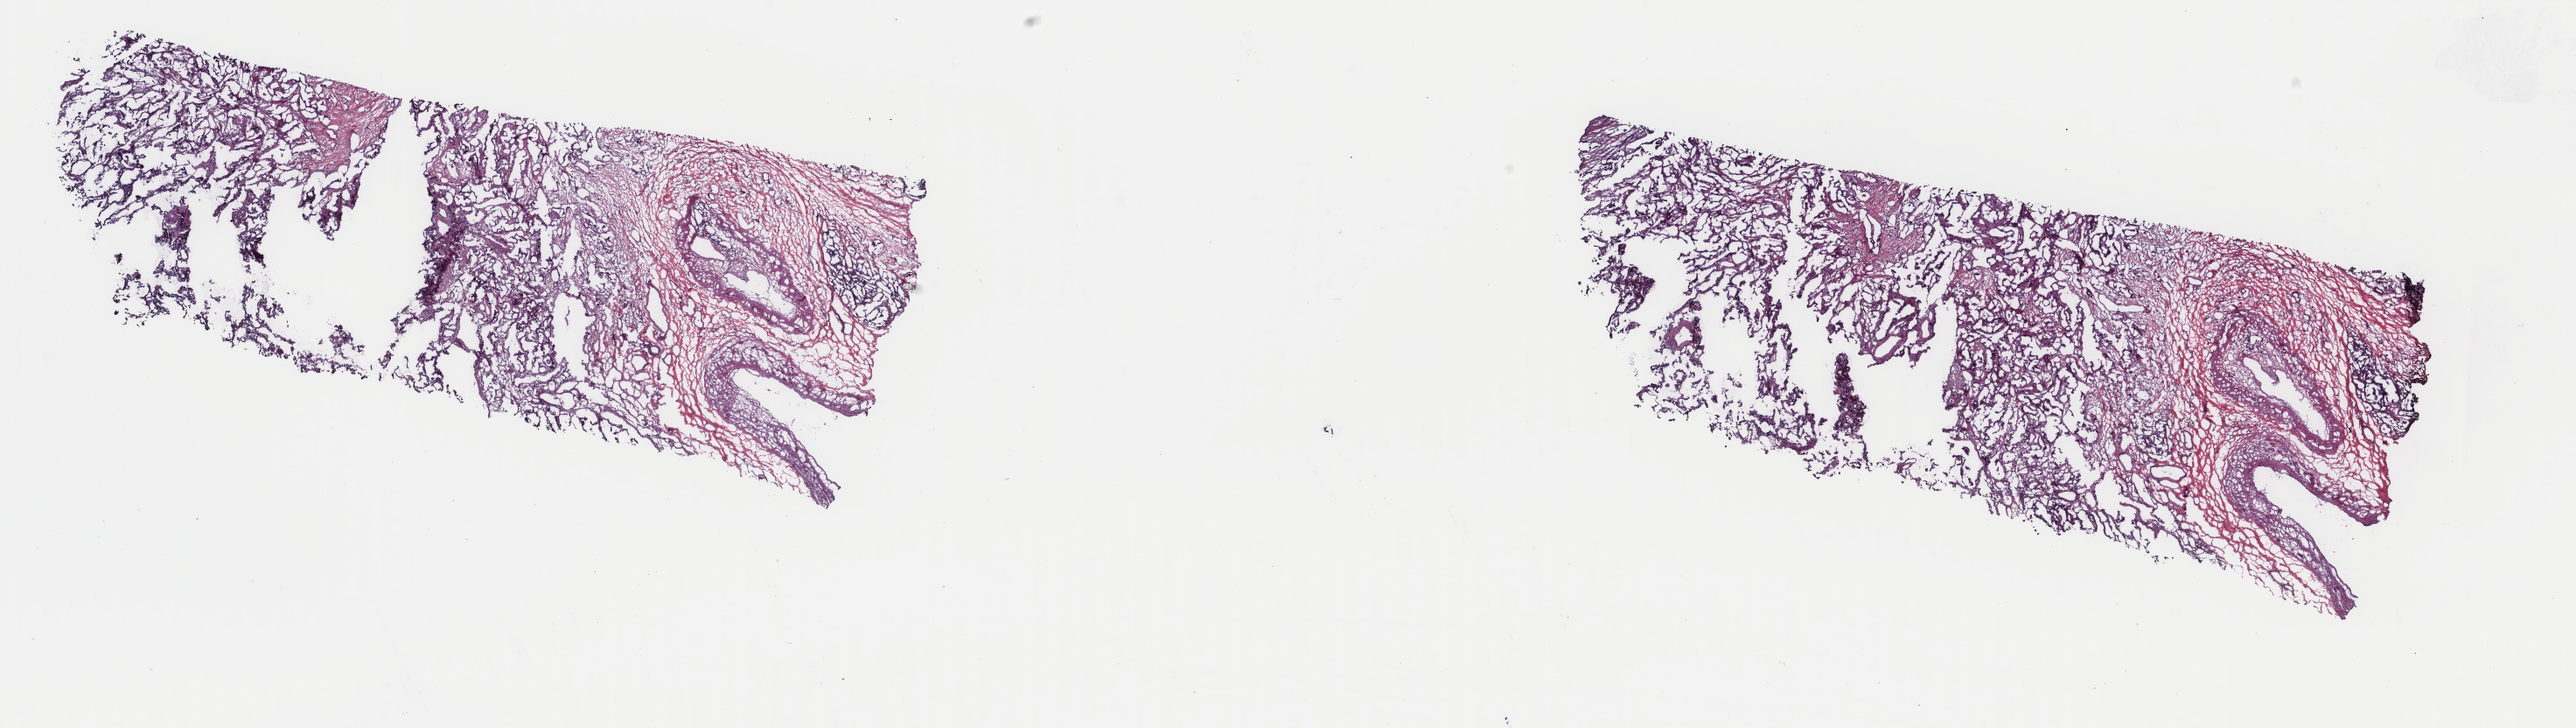
Digitized Hematoxylin and eosin (H&E) stained tissue section (whole slide) — low-resolution overview of the scanned area, about 23.4 x 6.6 mm, frozen section from the top of the tissue portion, sample: primary tumour, lung. Male, age 65 years at initial diagnosis. Pathologist review of this section (percent, as recorded): tumour cells 80%, tumour nuclei 75%, normal cells 0%, stromal cells 20%, necrosis 0%. Inflammatory infiltration, as recorded: lymphocyte infiltration 0%, monocyte infiltration 0%, neutrophil infiltration 0%.
* diagnosis: Adenocarcinoma with mixed subtypes (upper lobe, lung)
* laterality: left
* AJCC pathologic stage: IB (6th edition)